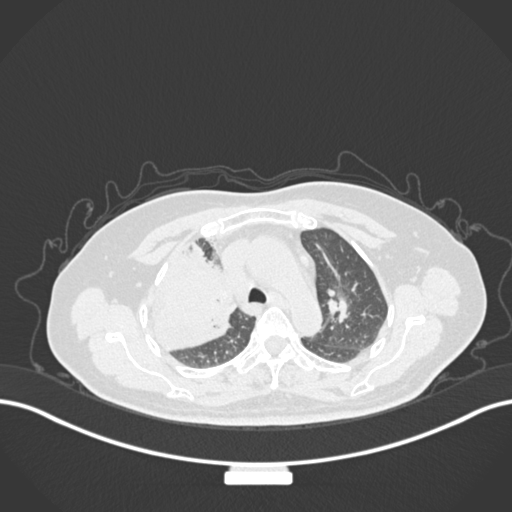
Chest CT, one axial slice. Slice 111 of 177 in the series (ordered by position). Lung window (W 1500 / L -600 HU). 1 mm slice thickness. 512 × 512 image matrix, field of view 400 × 400 mm. Female patient, age 60 years. From the clinical record (not read from this slice): clinical TNM (as recorded): T3 N1 M1.
Annotated regions visible in this slice (rectangle marked by the reading radiologist):
- lung tumour (recorded histology: adenocarcinoma): bounding box <137,247,231,354> (left, top, right, bottom; pixels)